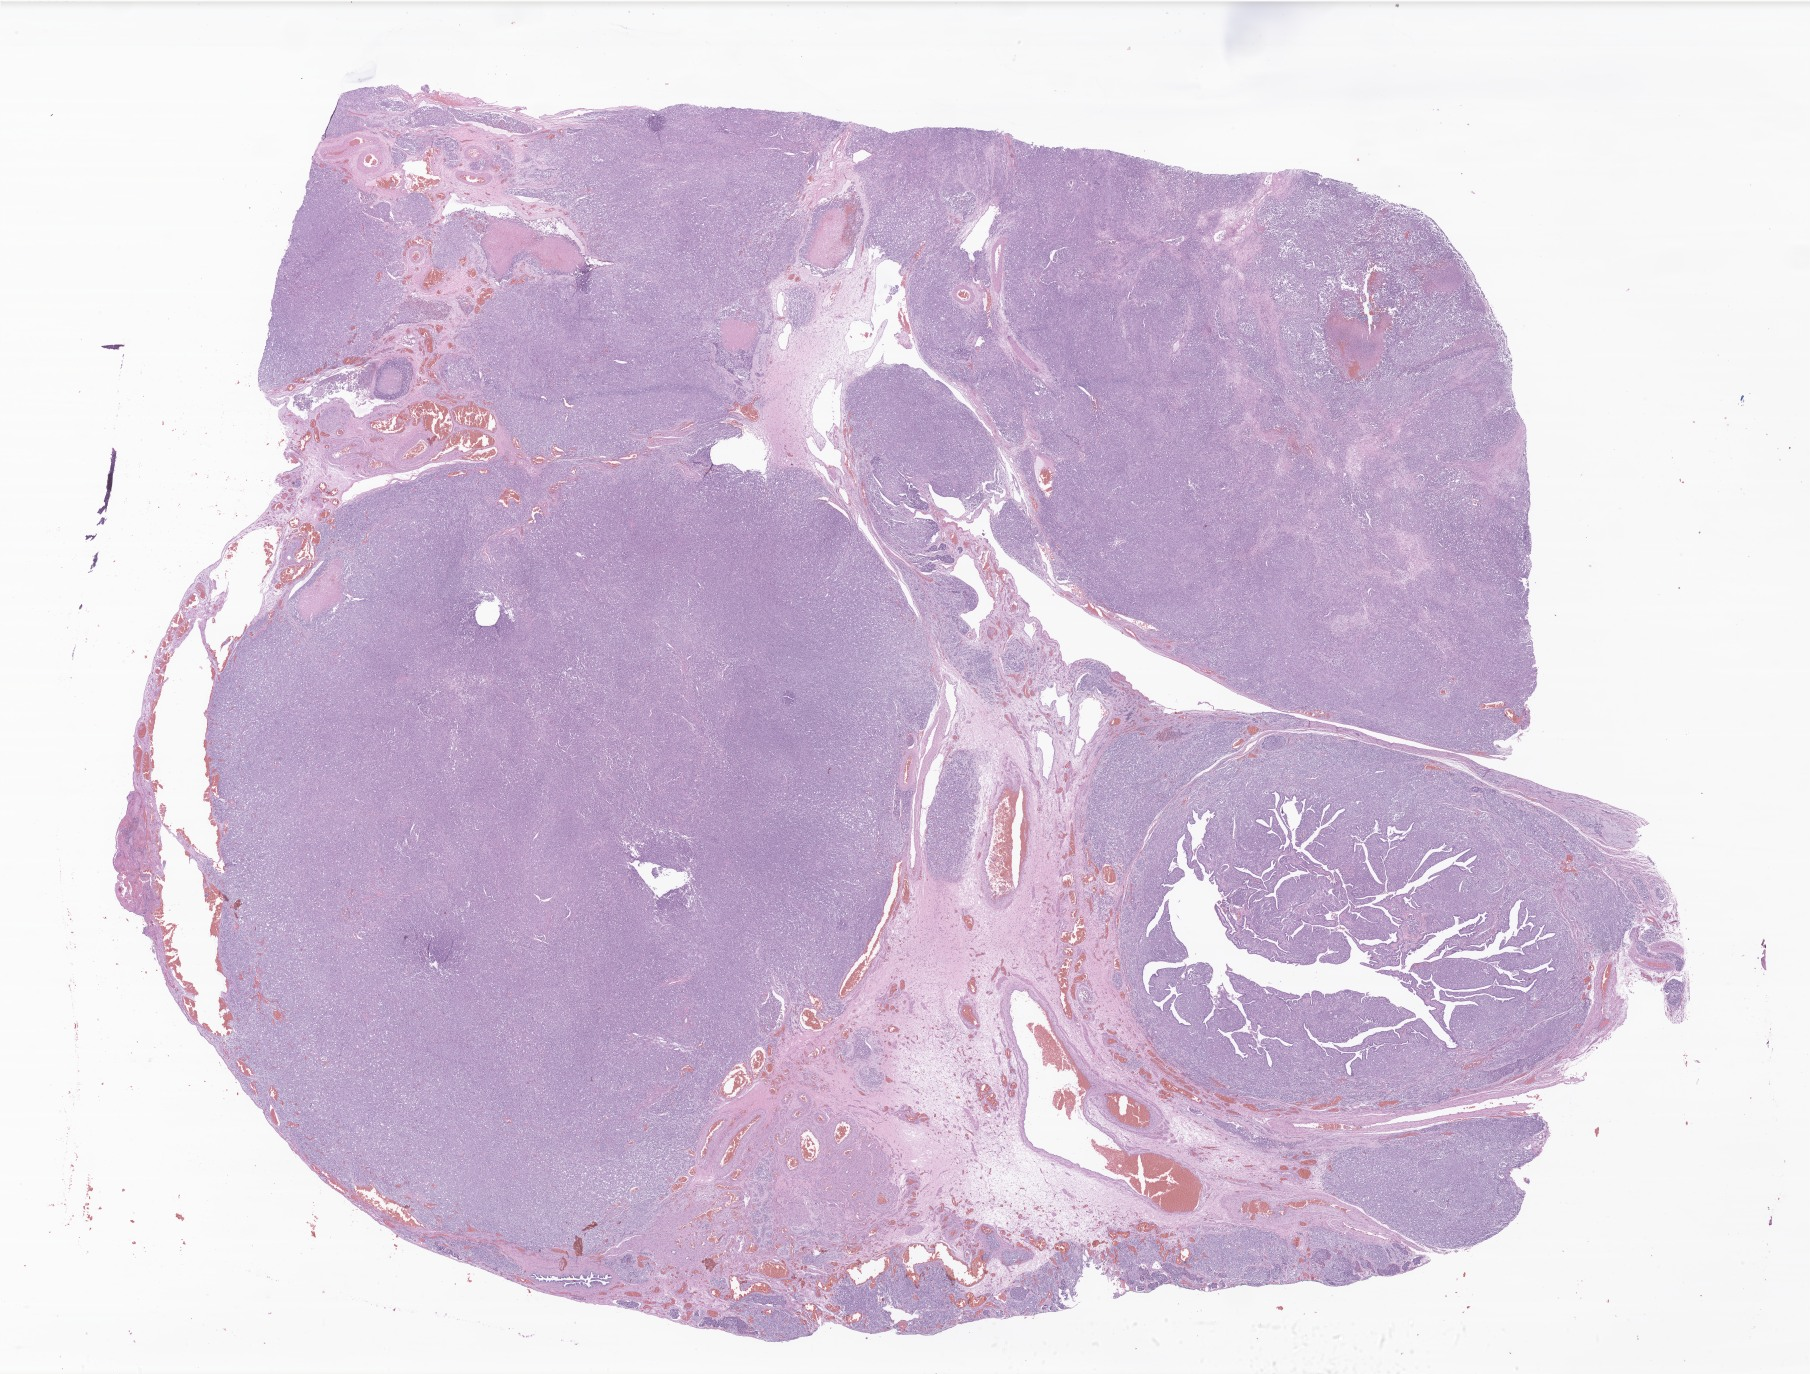
Digitized H&E-stained section of tumor tissue from the ovary — a low-resolution overview of the entire scanned area, about 30.5 x 23.2 mm, formalin-fixed, paraffin-embedded (FFPE) tissue. Patient: female, age 208 months.
* diagnosis: Small cell carcinoma, NOS